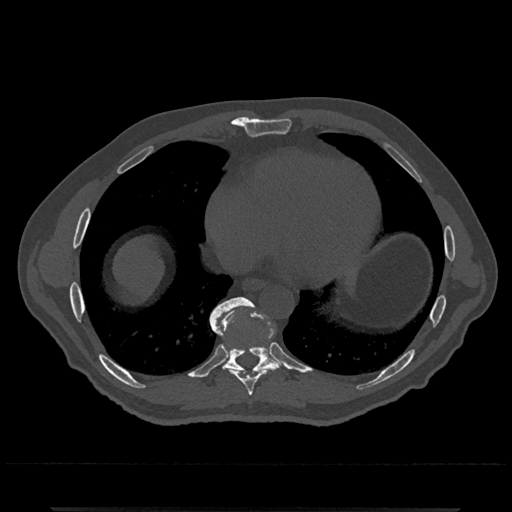
CT including the spine, one axial slice; slice 641 of 797 in the series (ordered by position); reconstruction kernel Br40s/3; 120 kVp; bone window (W 1800 / L 400 HU); 0.5 mm slice thickness; 512 × 512 image matrix, field of view 393 × 393 mm. Male patient, age 67 years. From the clinical record (not read from this slice): primary cancer: prostate.
Annotated regions visible in this slice (semi-automatic segmentation, software-assisted and operator-edited):
- T8 vertebra: box from (x=214, y=331) to (x=281, y=396) px
- T9 vertebra: (x=210, y=297)–(x=280, y=374)